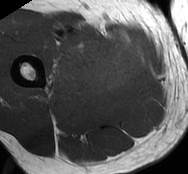
MRI of an extremity soft-tissue mass, one axial slice. Slice 28 of 93 in the series (ordered by position). MR volume resampled by the dataset authors to the PET/CT grid (not the native acquisition matrix). 3.27 mm slice thickness. 188 × 174 image matrix, field of view 184 × 170 mm. Male patient. From the clinical record (not read from this slice): histological type: undifferentiated - pleiomorphic; grade: high; site of the primary tumour: right thigh.
Outlined on this slice (expert contour drawn on MRI and transferred to this co-registered scan by the dataset authors):
- gross tumour volume including surrounding oedema: bounding box [x1, y1, x2, y2] px = [45, 27, 142, 98]
- gross tumour volume (mass): [81, 35, 142, 95]